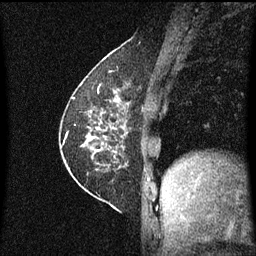
Breast MRI (dynamic contrast-enhanced), one sagittal slice; slice 23 of 60 in the series (ordered by position); dynamic contrast-enhanced series, image 2 of 3 at this slice position (ordered by acquisition); 1.5 T; TE 4.2 ms, TR 8.4 ms; 2 mm slice thickness; 256 × 256 image matrix, field of view 200 × 200 mm. Patient: female, 60 years.
Structures marked on this image (semi-automatic segmentation, software-assisted and operator-edited):
- analysis volume of interest (the breast-tissue region the enhancement analysis was run in; not a lesion): box from (x=69, y=66) to (x=135, y=193) px
- tumour enhancement mask (voxels above the 70 % enhancement threshold inside the analysis volume of interest): (x=87, y=96)–(x=129, y=165)